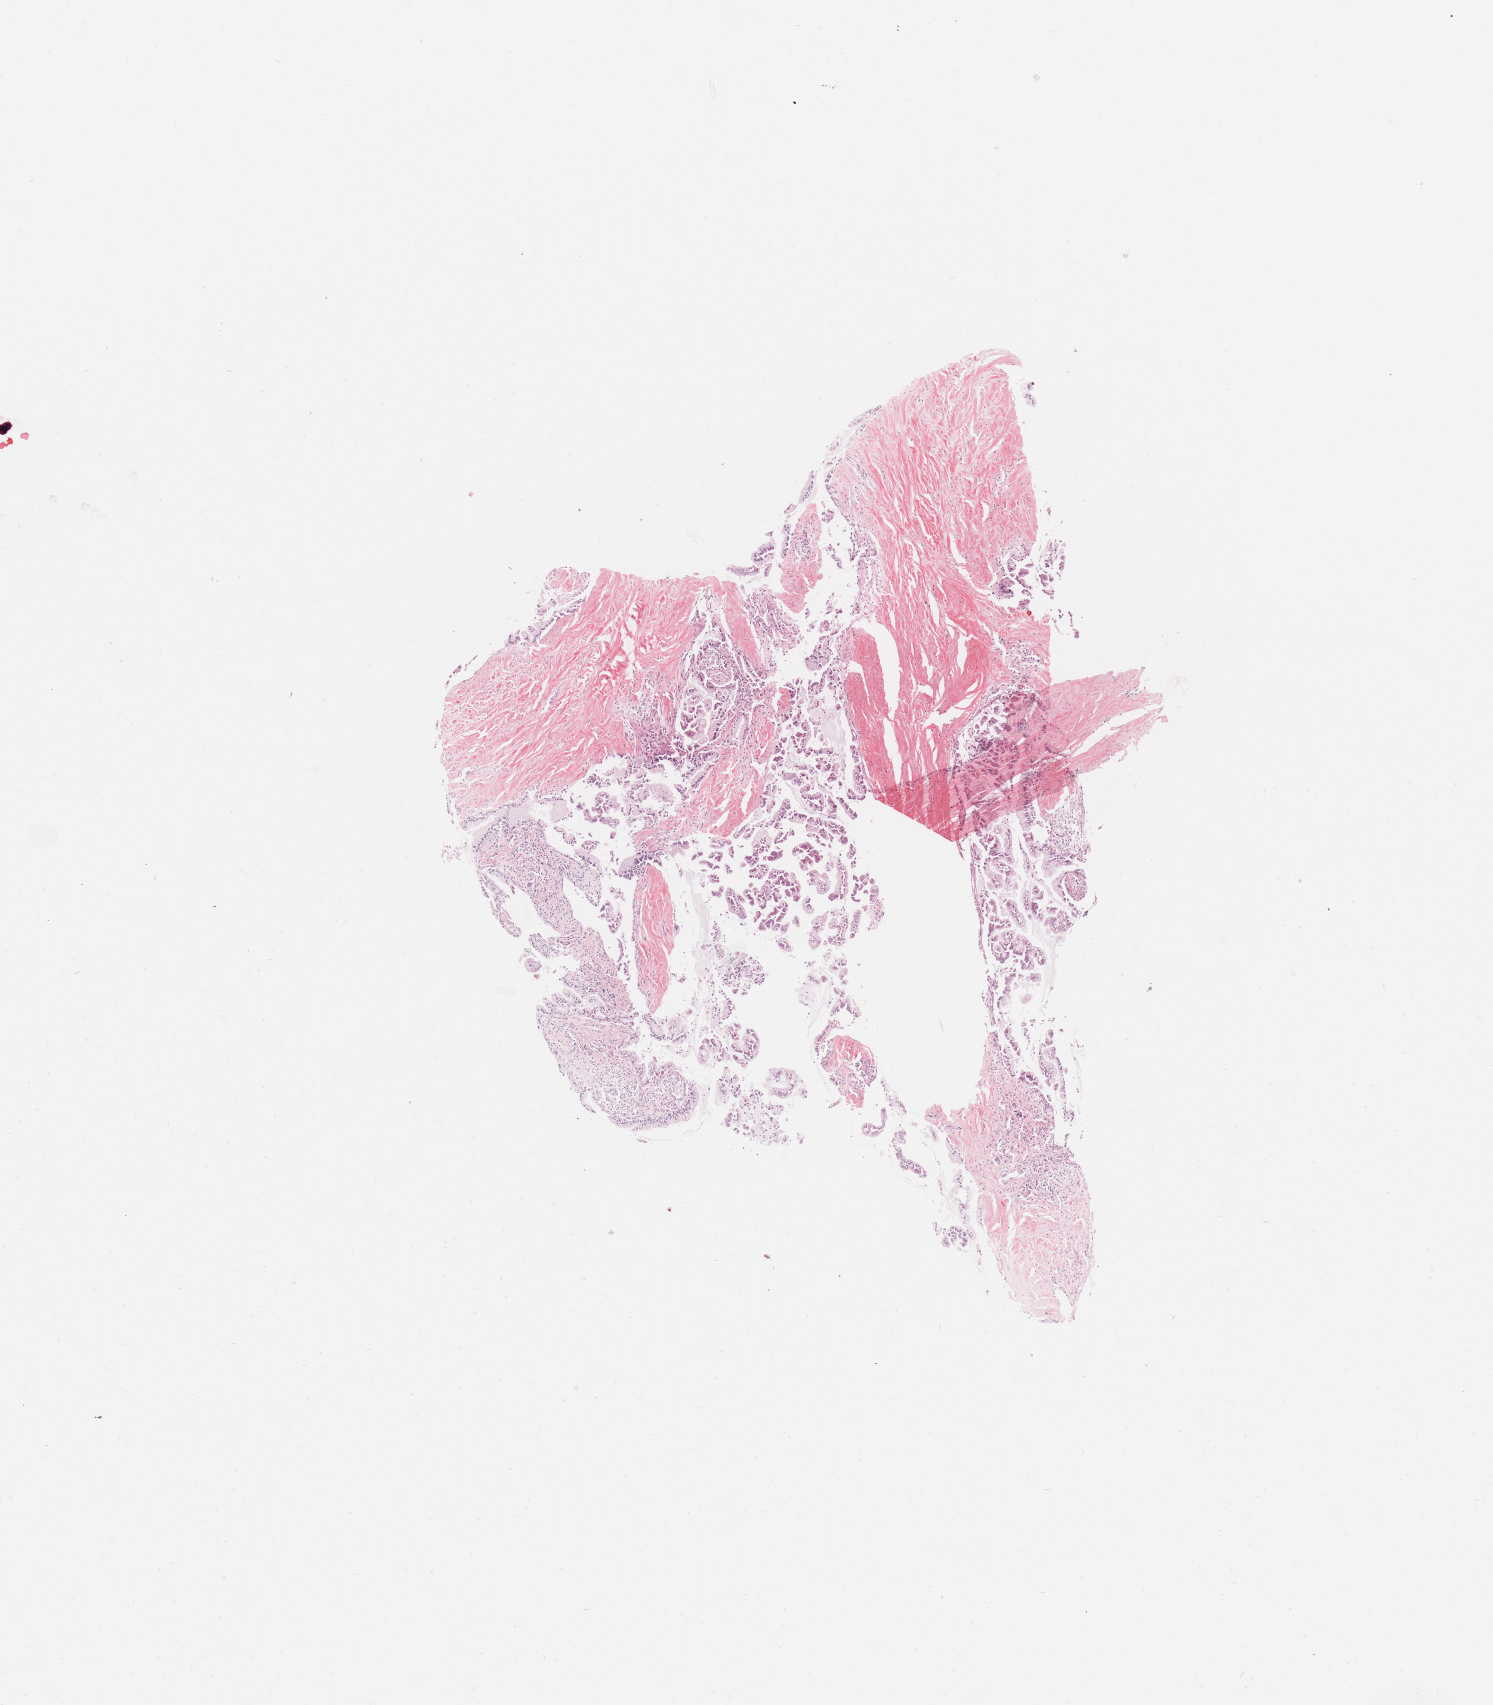
Hematoxylin and eosin (H&E) stained whole-slide image, whole scanned area (about 5.9 x 6.7 mm, from a 20x scan) shown as a low-resolution overview, tumour tissue sample, sampled site: pancreas. Female, 54 y/o. Composition of this section per pathologist review: tumour nuclei 30%, necrosis 0%.
Diagnosis: Infiltrating duct carcinoma, NOS.